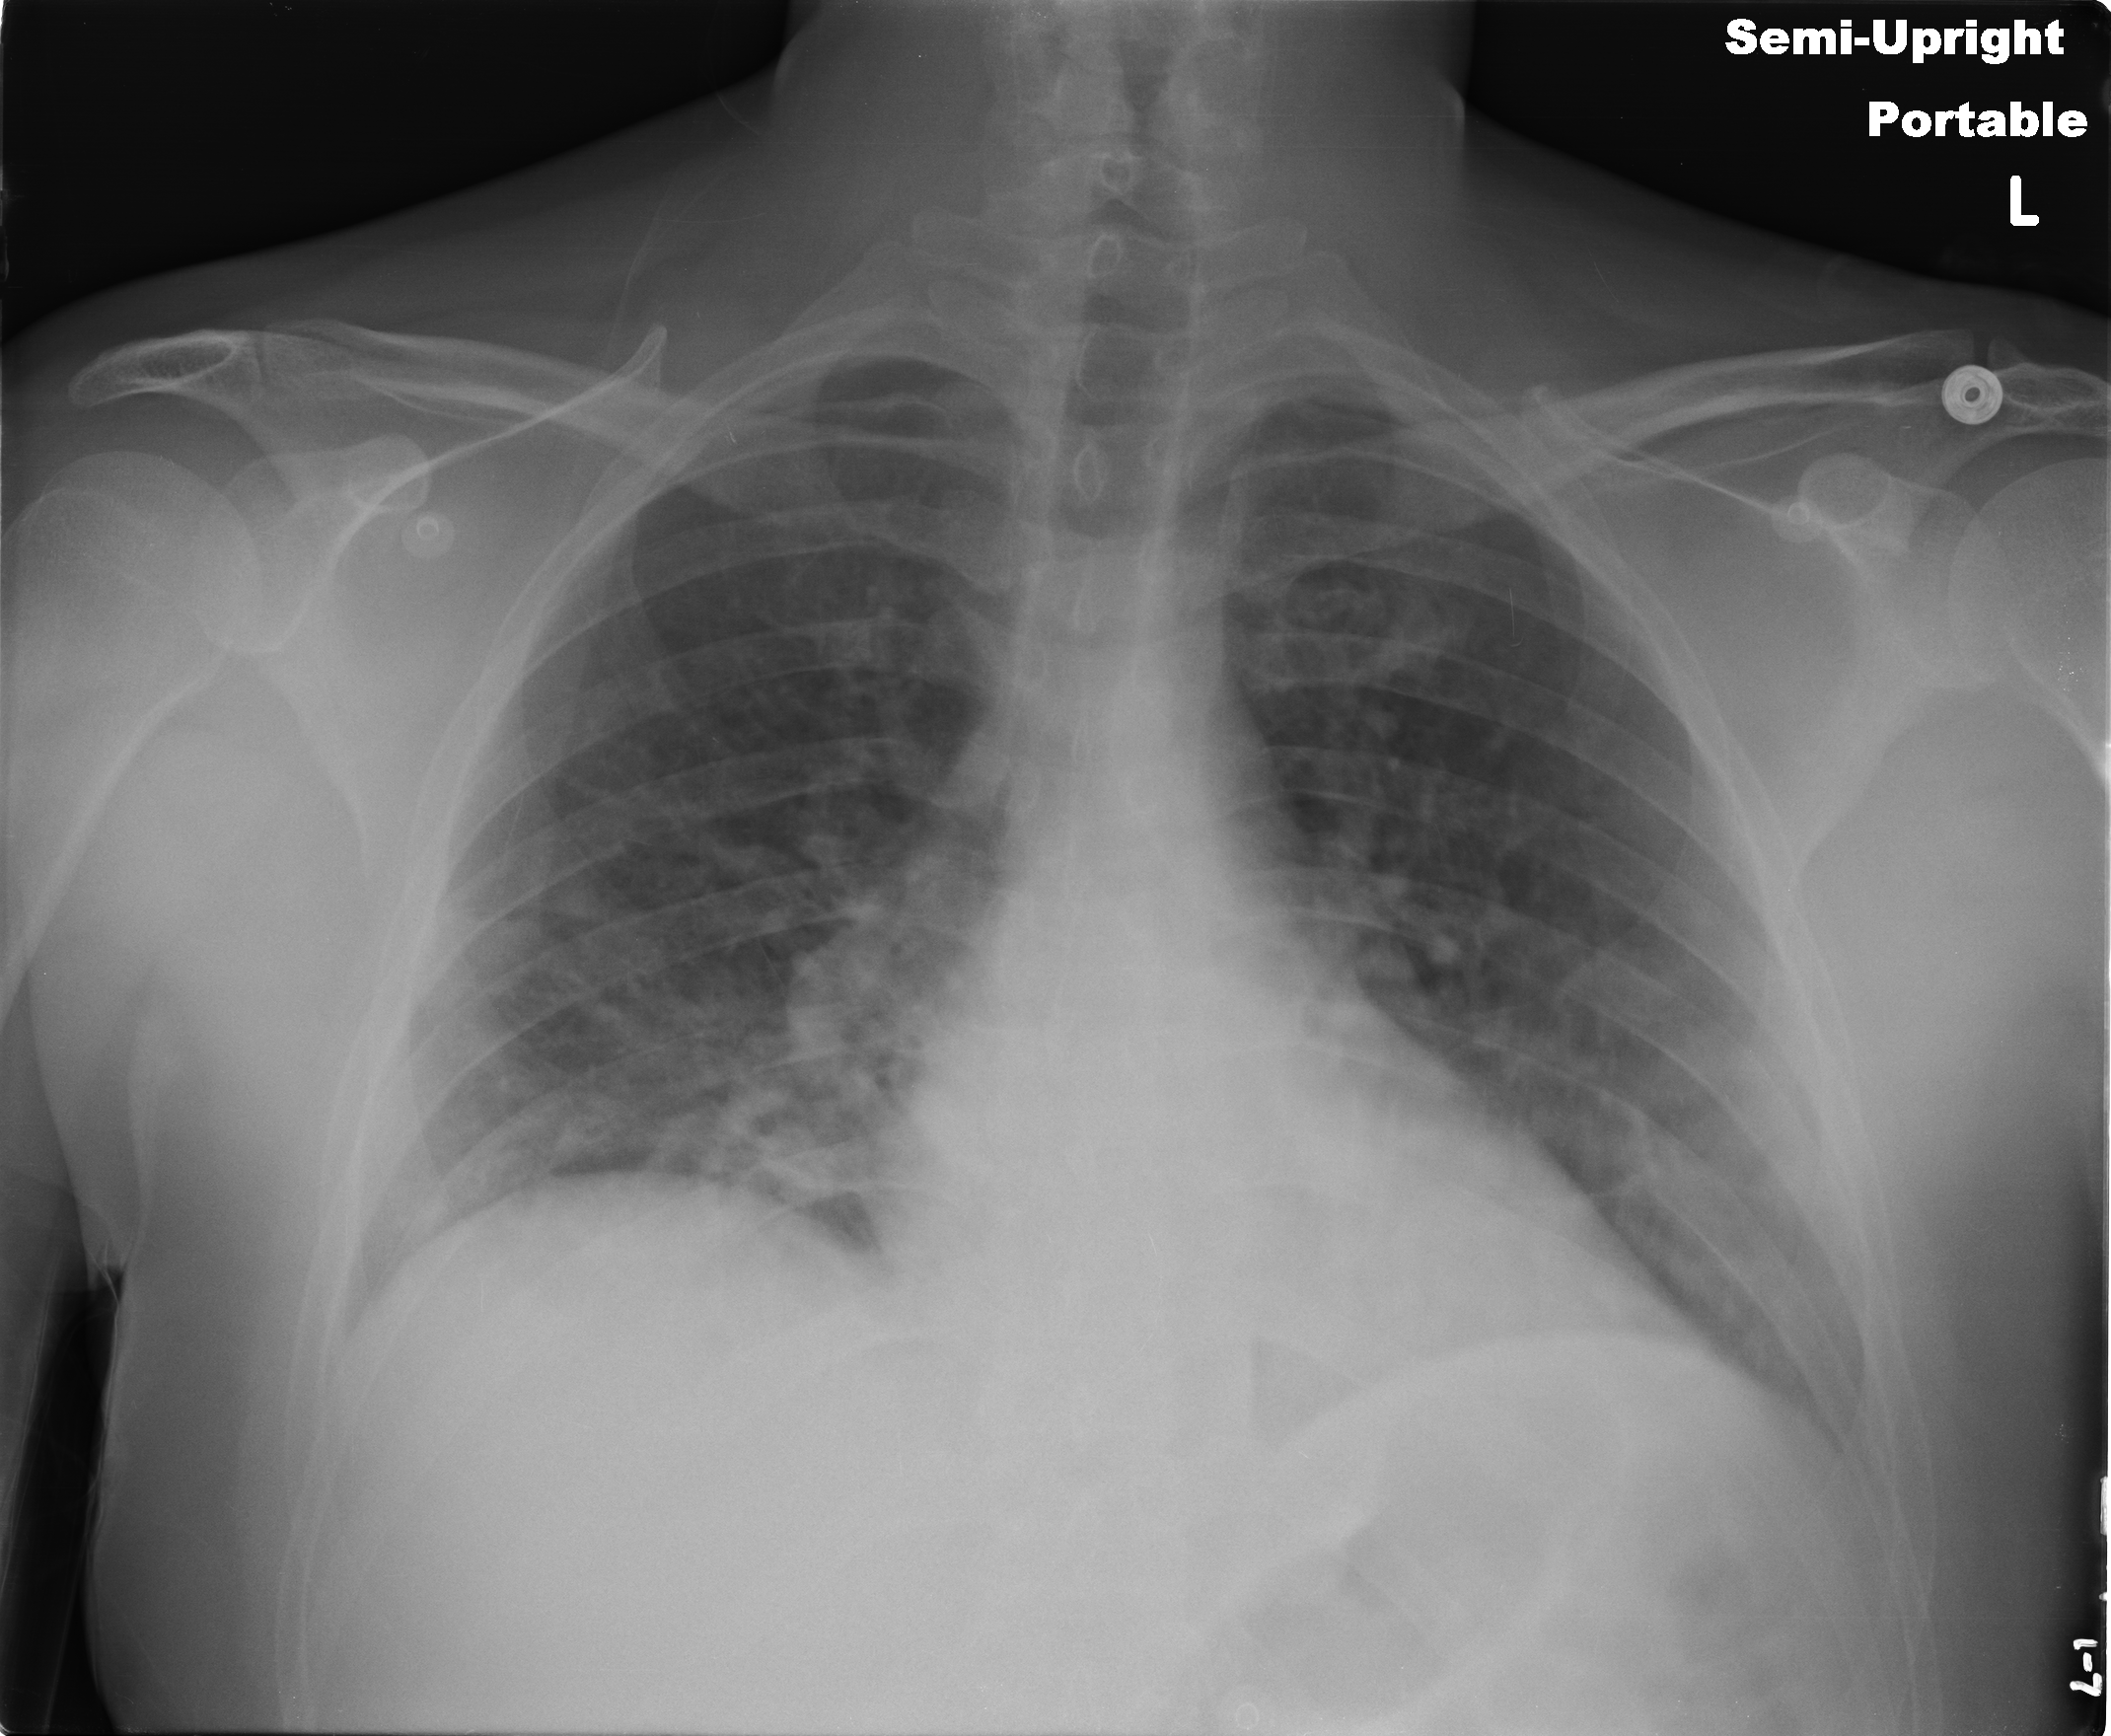
Portable chest radiograph, AP projection. Male patient, age 37 years; imaged 0 days after the COVID-19 diagnosis.
Radiologist key findings (as recorded): mild bibasilar airspace opacities.